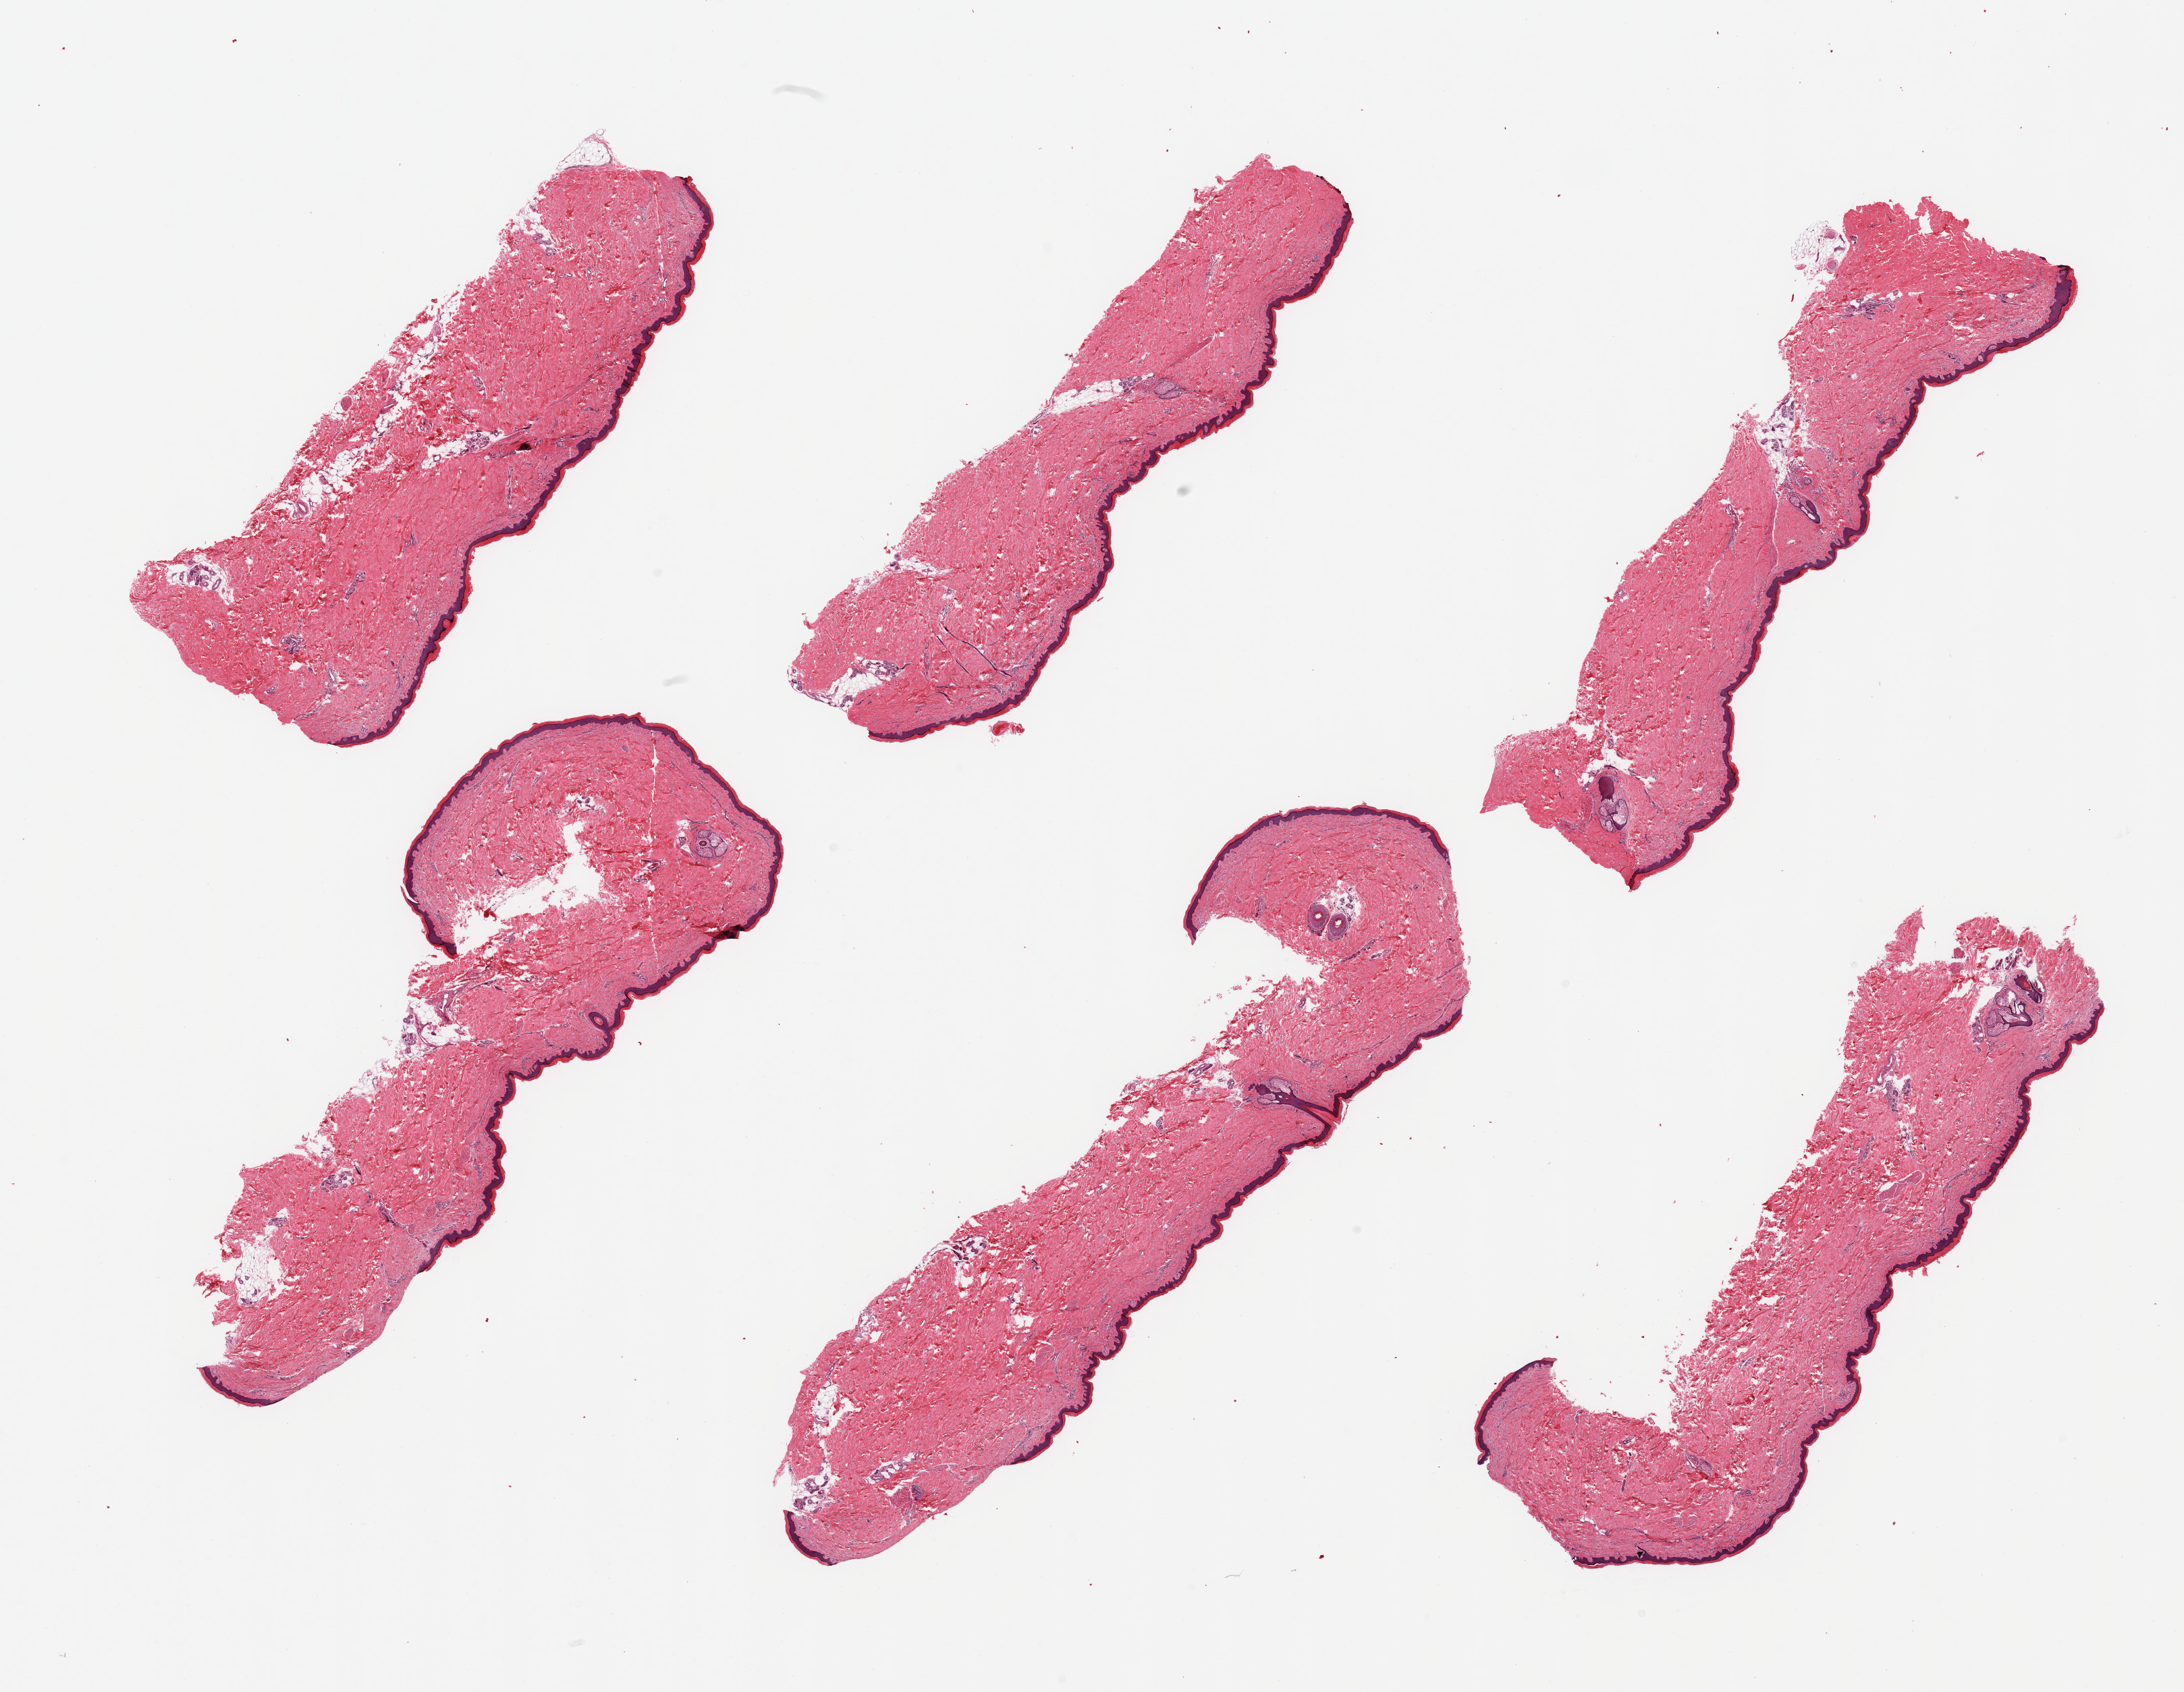
Digitized hematoxylin and eosin (H&E)-stained section, a low-resolution overview of the entire scanned area, about 25.6 x 19.8 mm; PAXgene-fixed paraffin-embedded (PFPE) section; sampled site (target tissue): skin of lower leg; tissue donor sample. Male donor.
• pathologist's review note for this sample: 6 pieces, squamous epithelium is ~60 microns; minimal dermal fat